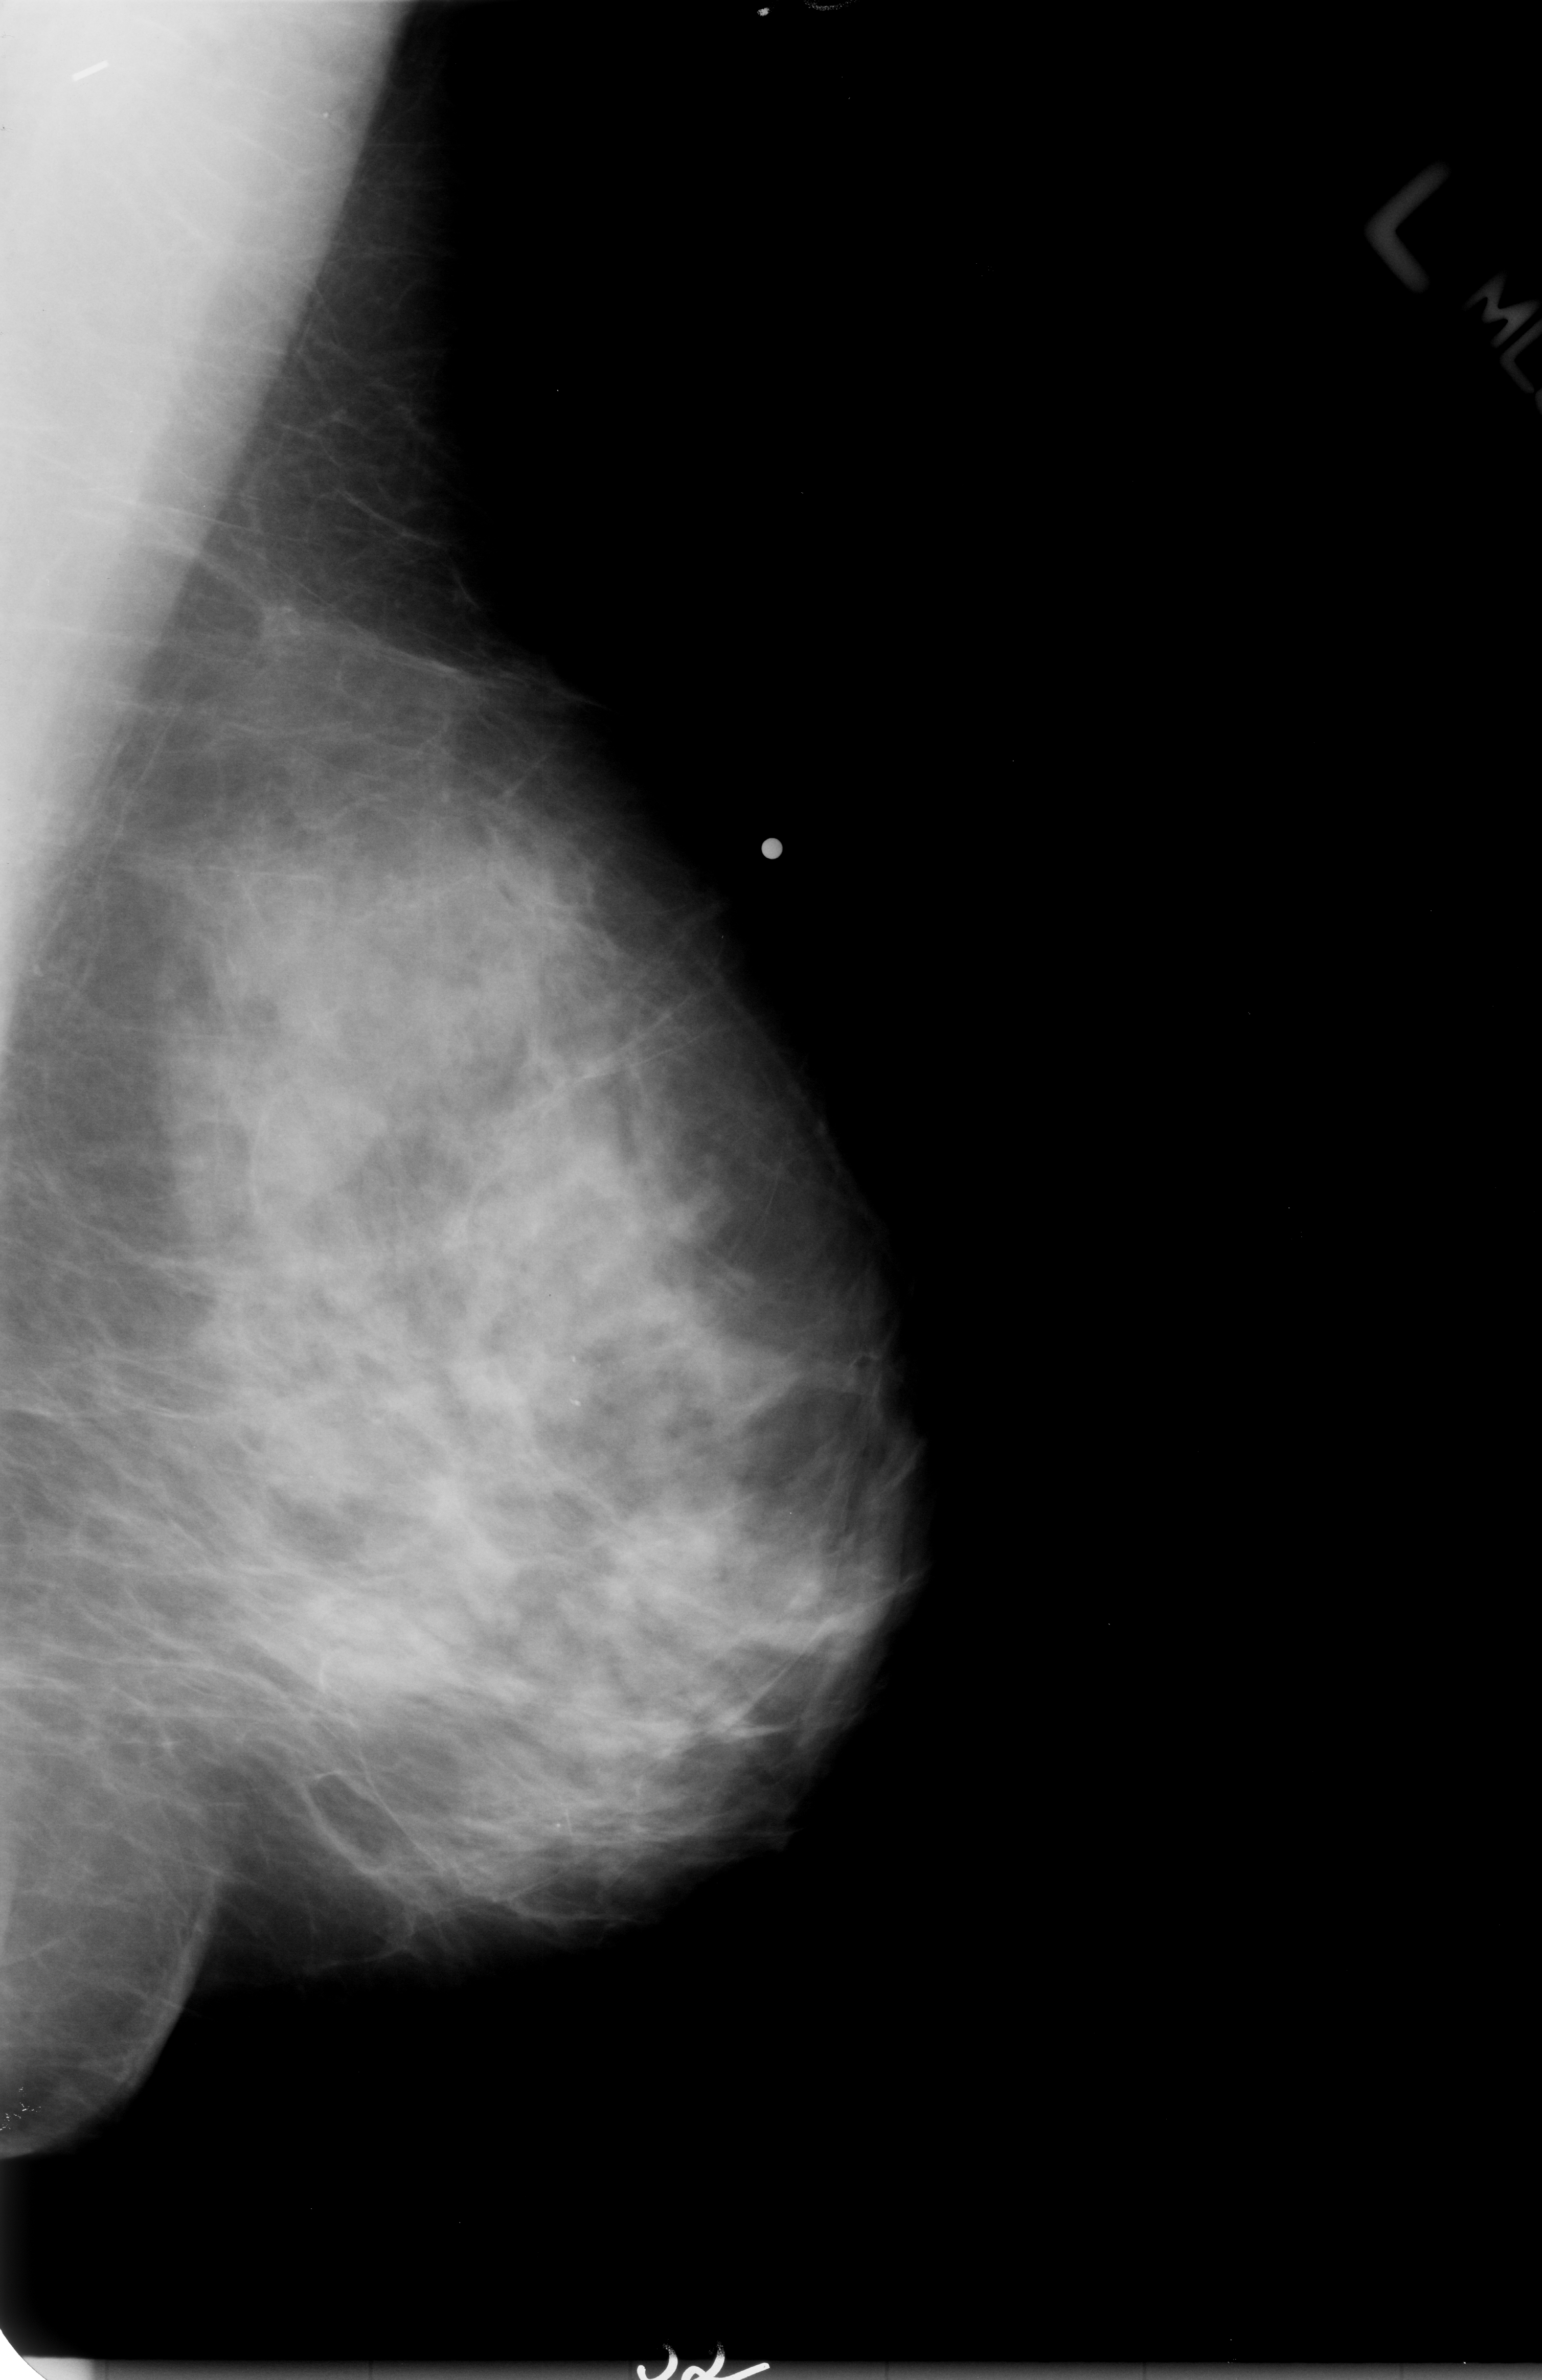
Scanned film-screen mammogram; left breast; MLO view.
- Finding: mass, shape irregular, margins obscured / ill defined; BI-RADS assessment category 3; subtlety rating 3 on a 1 (subtle) to 5 (obvious) scale; pathology result (as recorded, not read from the image): malignant.